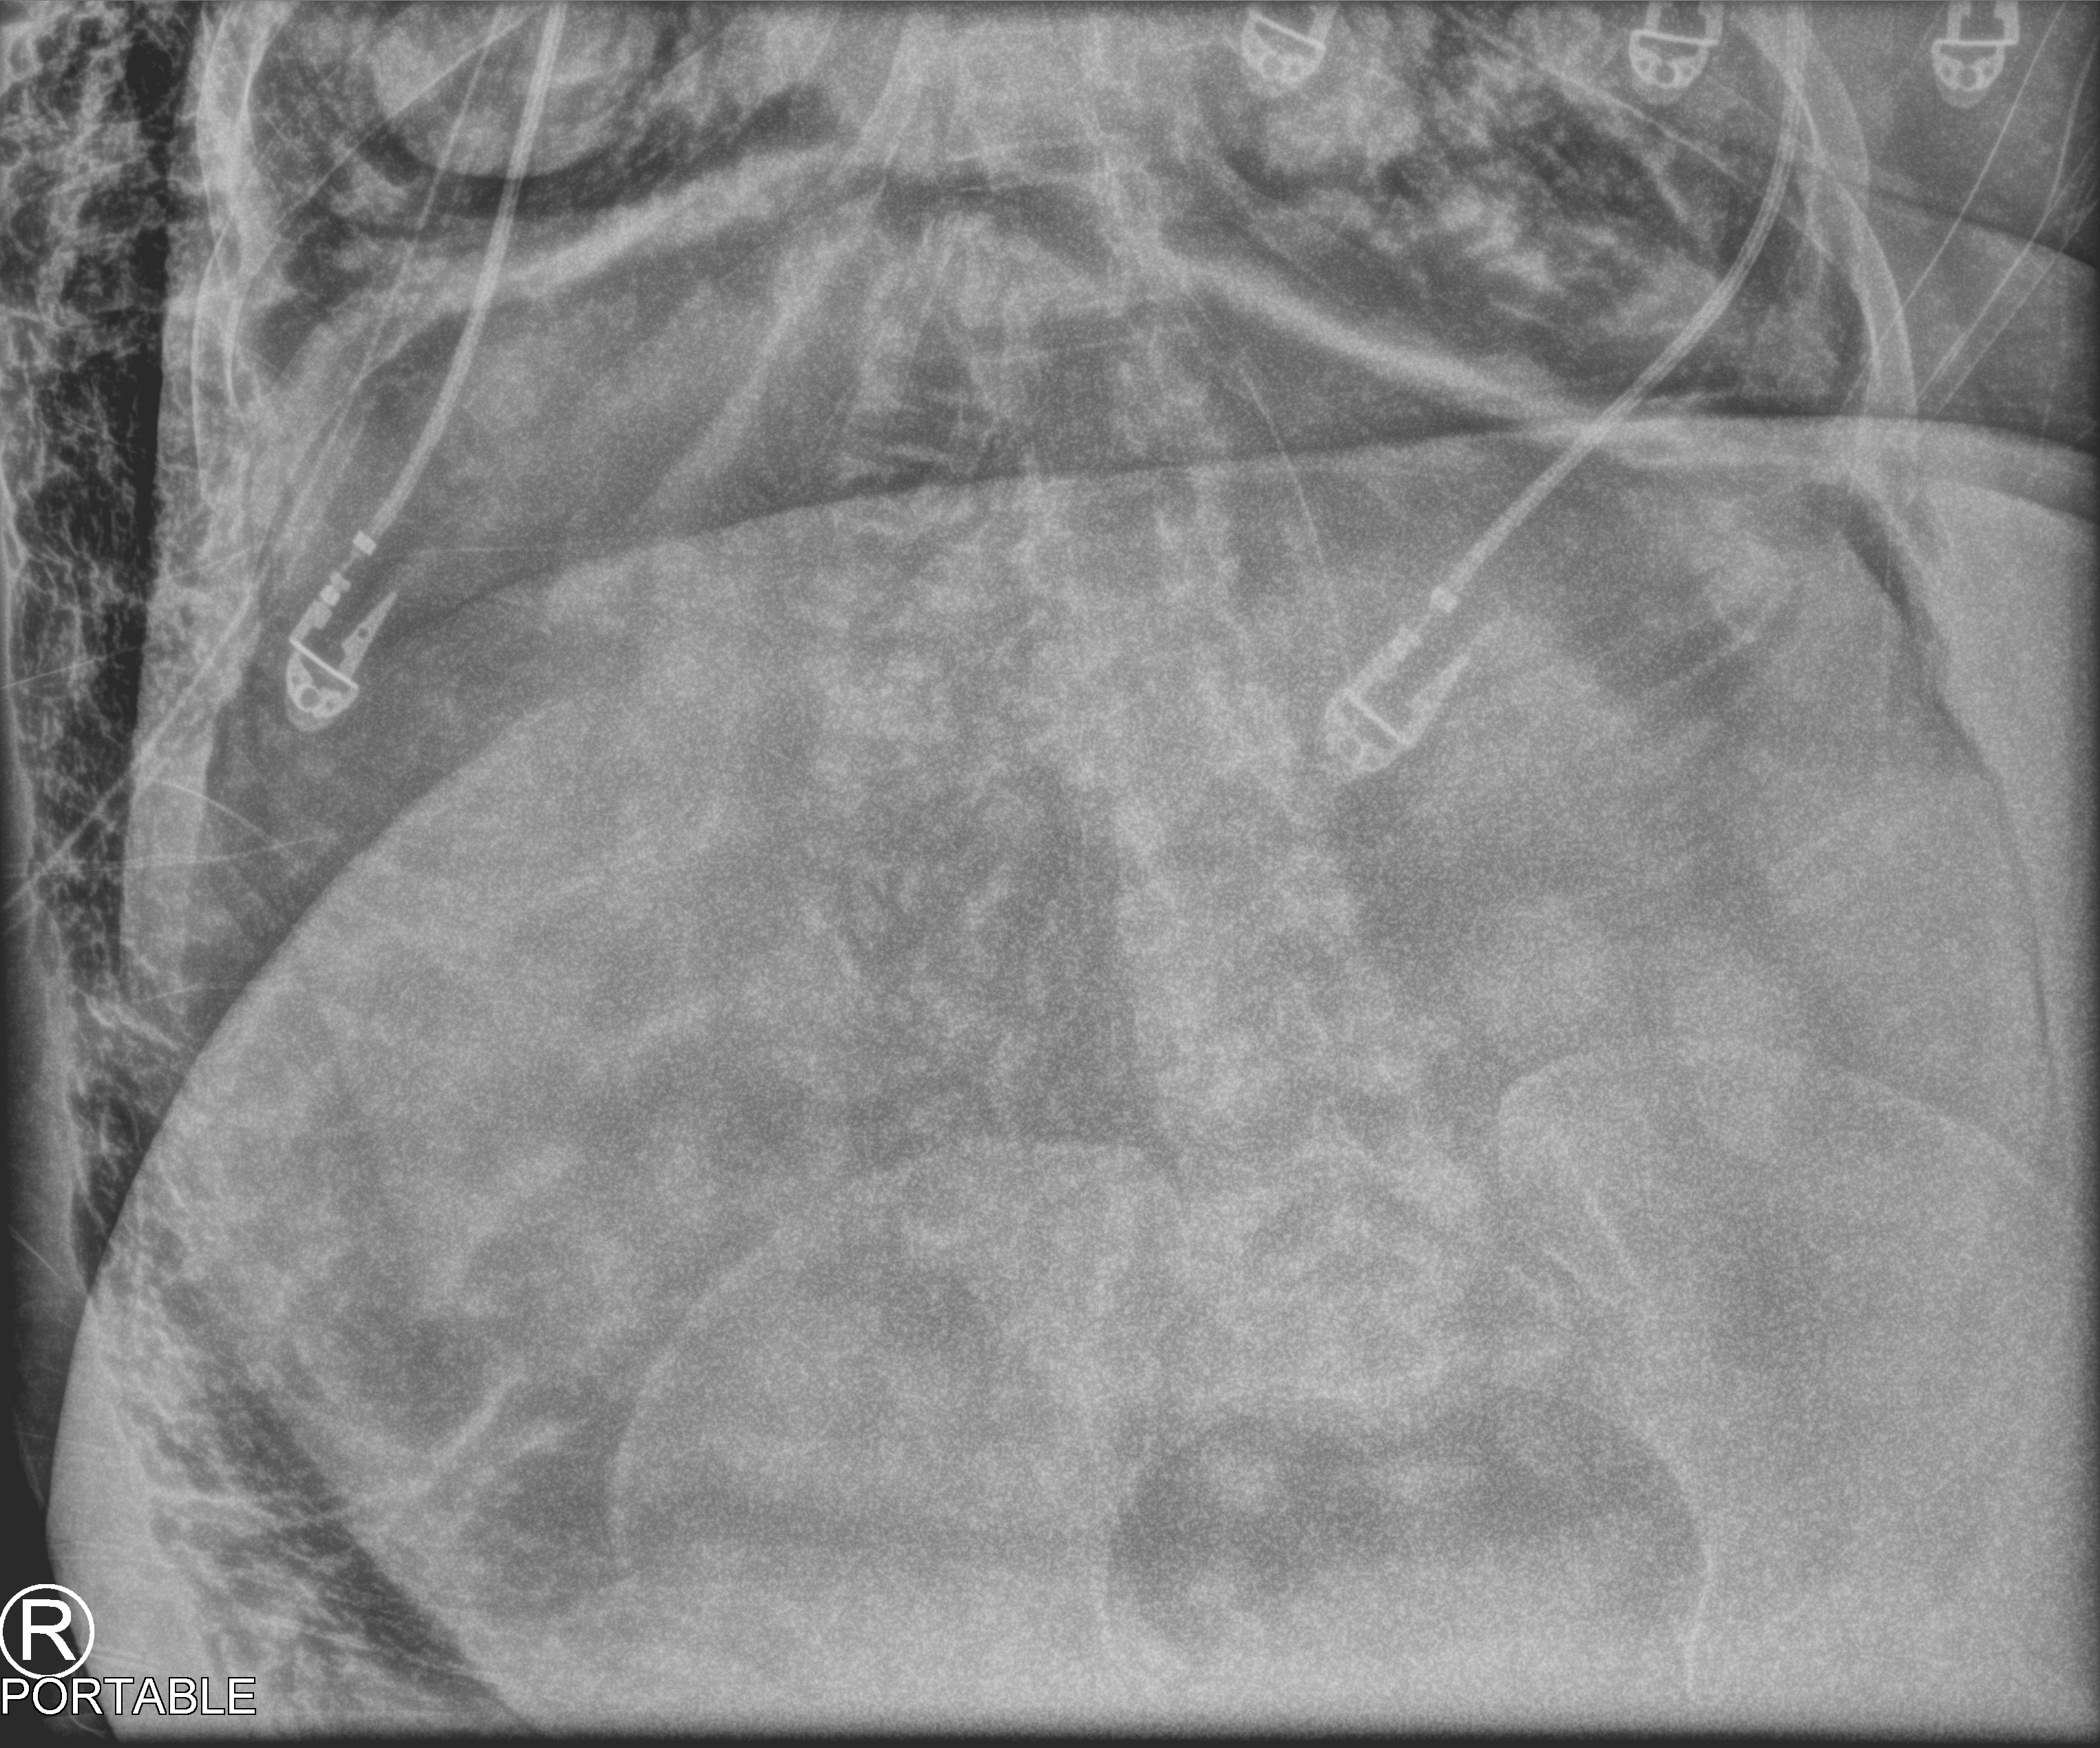
Abdomen X-ray (portable), anteroposterior (AP) projection. Patient hospitalised with COVID-19, aged 18–59 years.
From the hospital-stay record, not from the radiograph (when in the stay this image was taken is not recorded):
- COPD (admission record): no
- admitted to intensive care during this hospital stay: yes